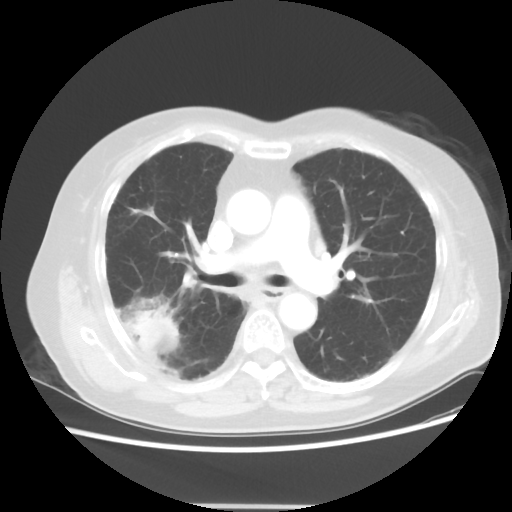
Chest CT, one axial slice. Slice 29 of 50 in the series (ordered by position). Reconstruction kernel STANDARD. Lung window (W 1500 / L -600 HU). 5 mm slice thickness. 512 × 512 image matrix, field of view 360 × 360 mm. Female patient, age 72 years. Case-level facts recorded for this patient, not image findings: clinical TNM (as recorded): T2 N1 M0; histopathological grade: G1.
Structures marked on this image (rectangle marked by the reading radiologist):
- lung tumour (recorded histology: adenocarcinoma): bounding box (x1, y1, x2, y2) in pixels: (129, 310, 180, 351)